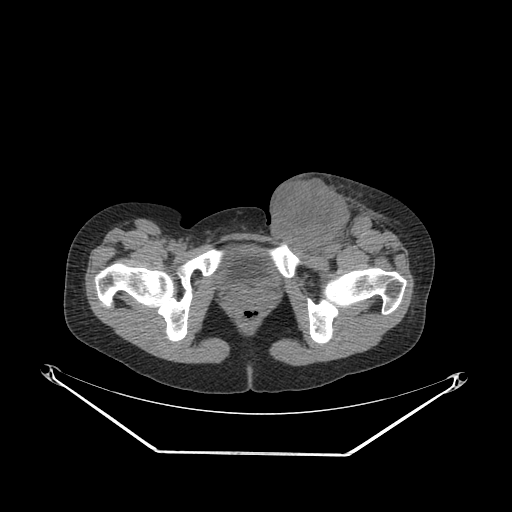
CT of an extremity soft-tissue mass (from a PET/CT study), one axial slice. Slice 65 of 267 in the series (ordered by position). 140 kVp. Soft-tissue window (W 400 / L 40 HU). 3.75 mm slice thickness. 512 × 512 image matrix, field of view 500 × 500 mm. Female patient. Case-level facts recorded for this patient, not image findings: histological type: leiomyosarcoma; grade: high; site of the primary tumour: groin.
Structures marked on this image (expert contour drawn on MRI and transferred to this co-registered scan by the dataset authors):
- gross tumour volume including surrounding oedema: bounding box (x1, y1, x2, y2) in pixels: (262, 176, 387, 254)
- gross tumour volume (mass): (263, 180, 348, 254)